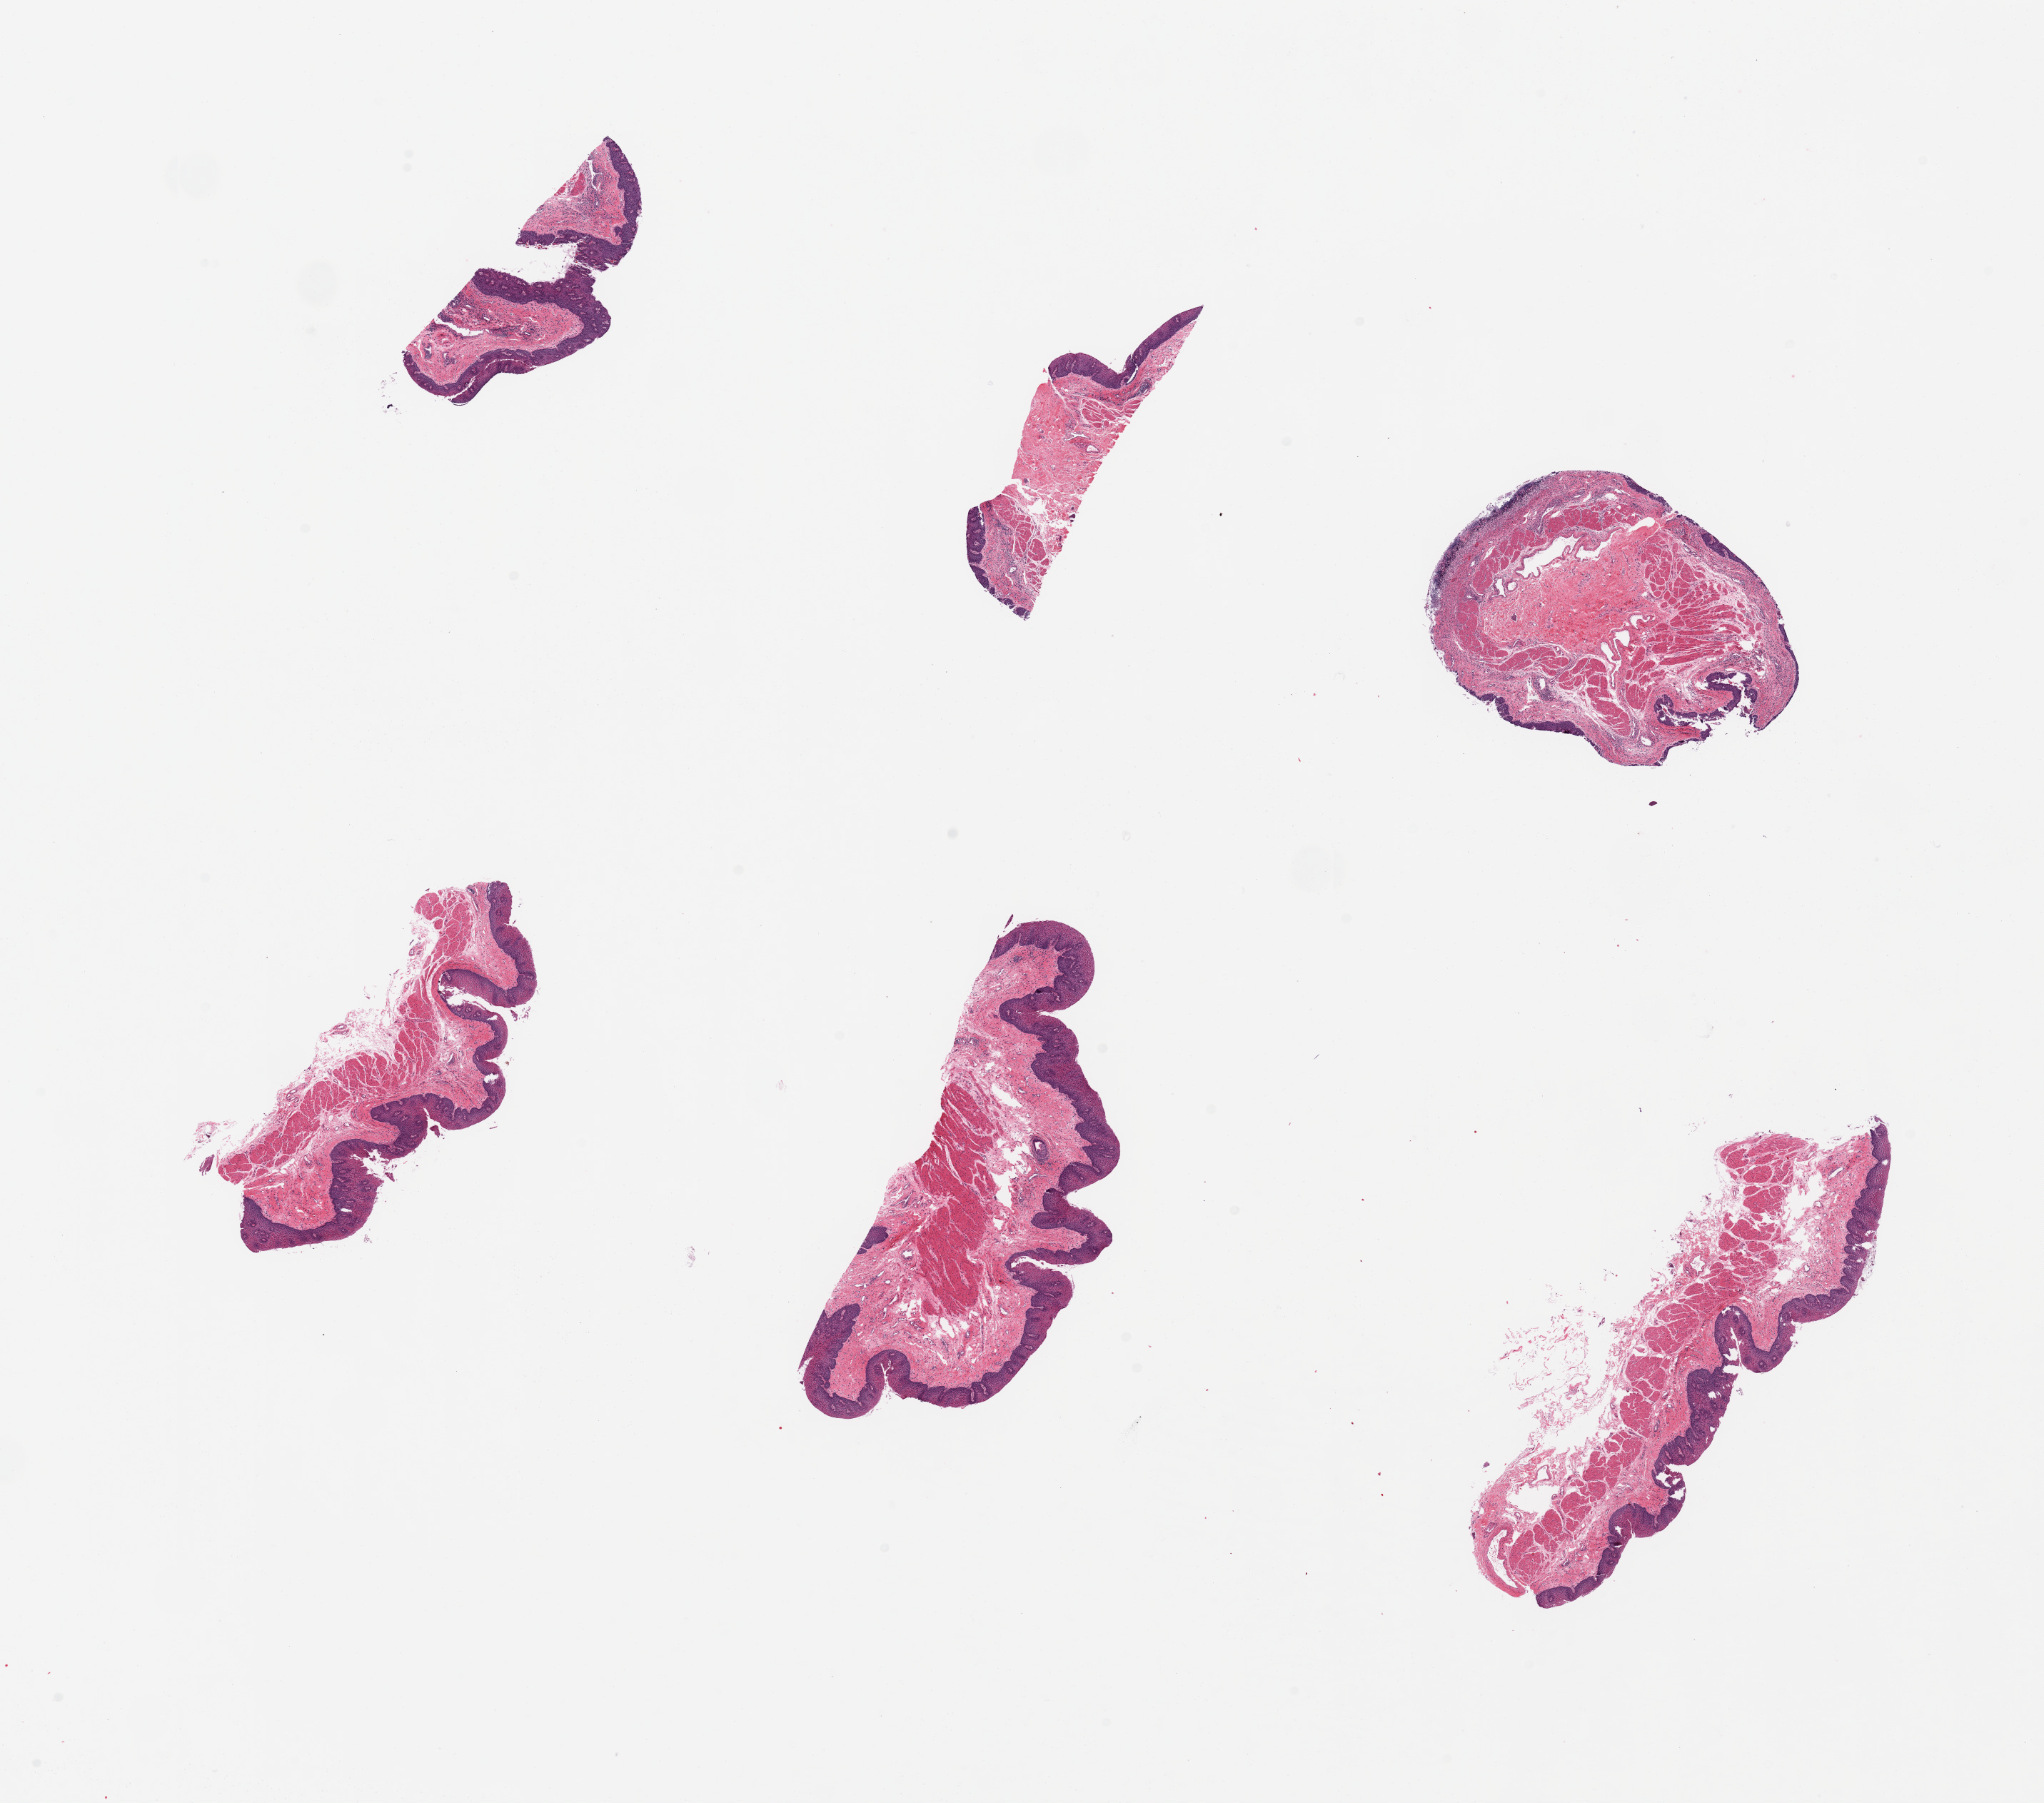
Digitized haematoxylin and eosin-stained section, shown as a low-resolution overview of the whole scanned area (about 22.6 x 20.0 mm); PAXgene-fixed, paraffin-embedded tissue; sampled site (target tissue): esophageal mucous membrane; donor tissue sample.
Review note (as recorded): 6 pieces, erosive esophagitis, probably fungal.